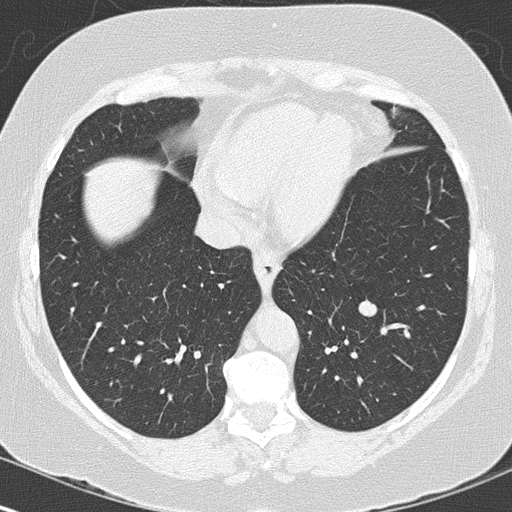
Axial slice from a low-dose chest CT screening exam. Baseline screening round. Lung window (W 1500 / L -600 HU). Lung (sharp) reconstruction kernel (B50f). 512 × 512 image matrix. Female, age 60 years at enrolment. Former smoker at enrolment.
Lesion marked by an expert reader, bounding box (x1, y1, x2, y2) in pixels: (349, 291, 391, 331). The exam's reader record, not a measurement of the box and not confirmed to be the same lesion: non-calcified nodule or mass ≥4 mm, left lower lobe, 12 × 10 mm, smooth margins, soft tissue attenuation. Official screen result: positive, change unspecified: nodule(s) >= 4 mm or enlarging nodule(s), mass(es), or other non-specific abnormalities suspicious for lung cancer.